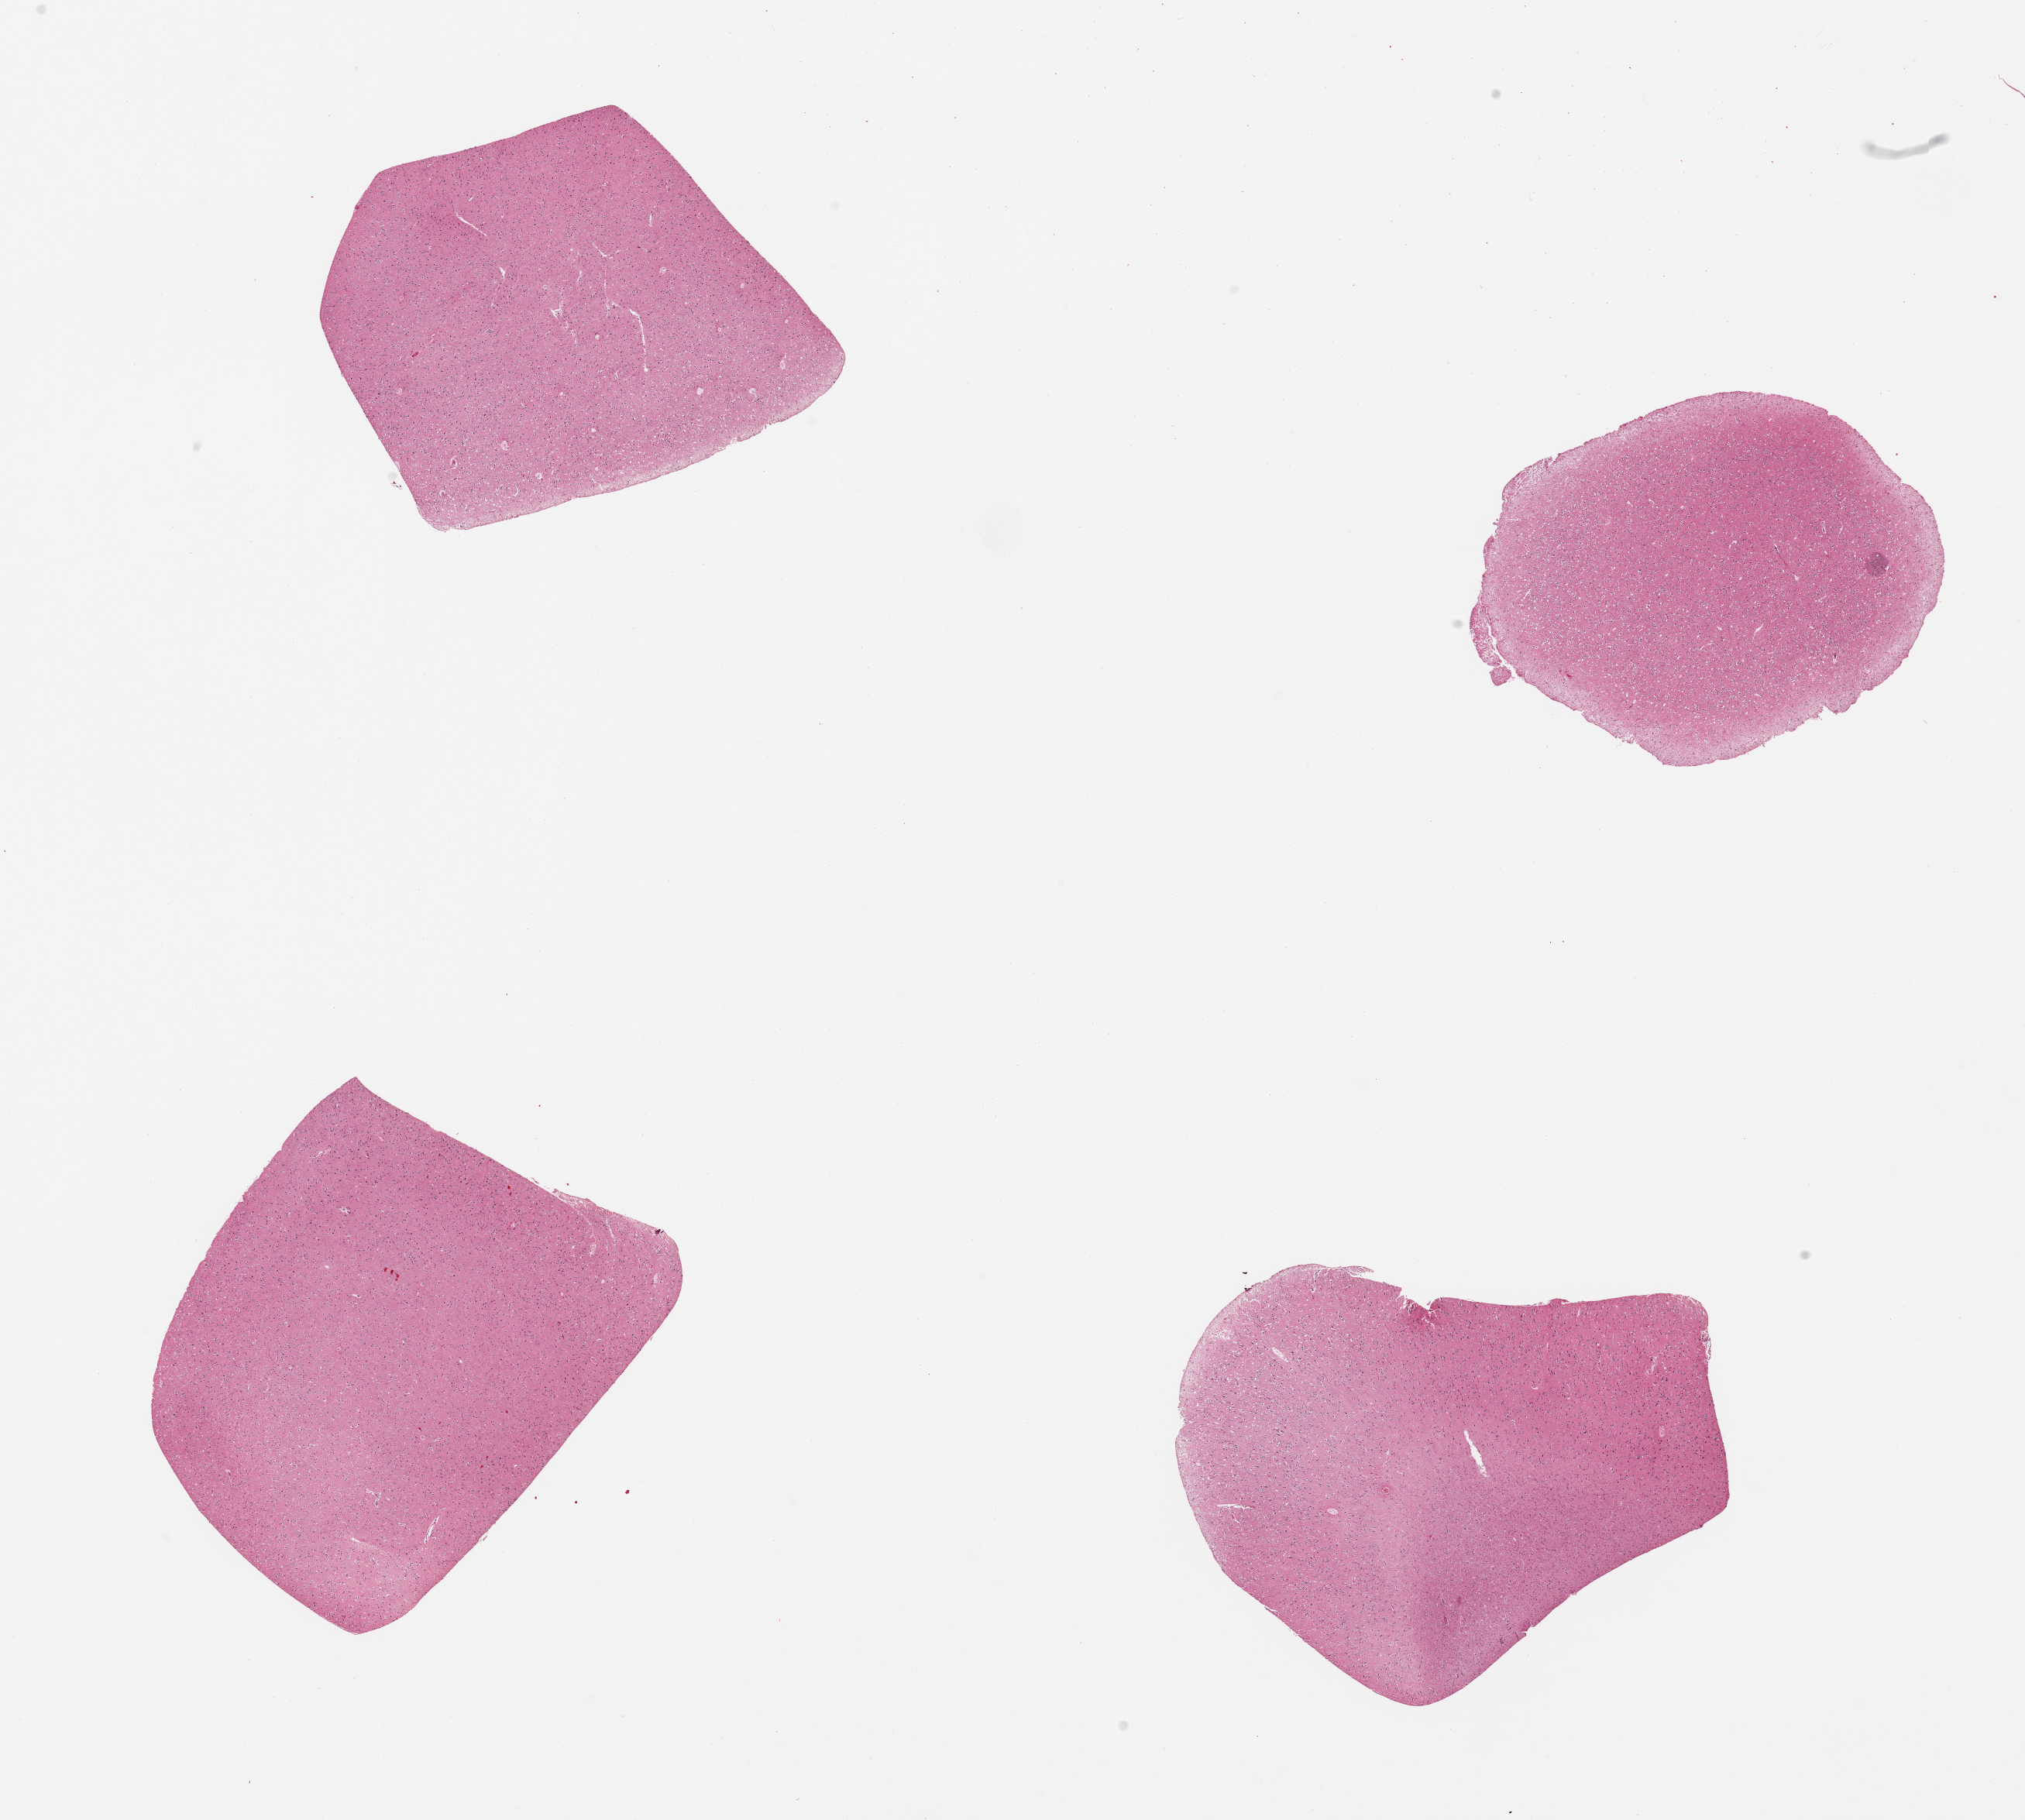
H&E whole-slide image — whole scanned area (about 20.7 x 18.6 mm, acquisition: 20x scan) shown as a low-resolution overview. PAXgene-fixed, paraffin-embedded tissue. Target tissue: cerebral cortex. Tissue donor sample. Male donor.
Review note (as recorded): 4 pieces.